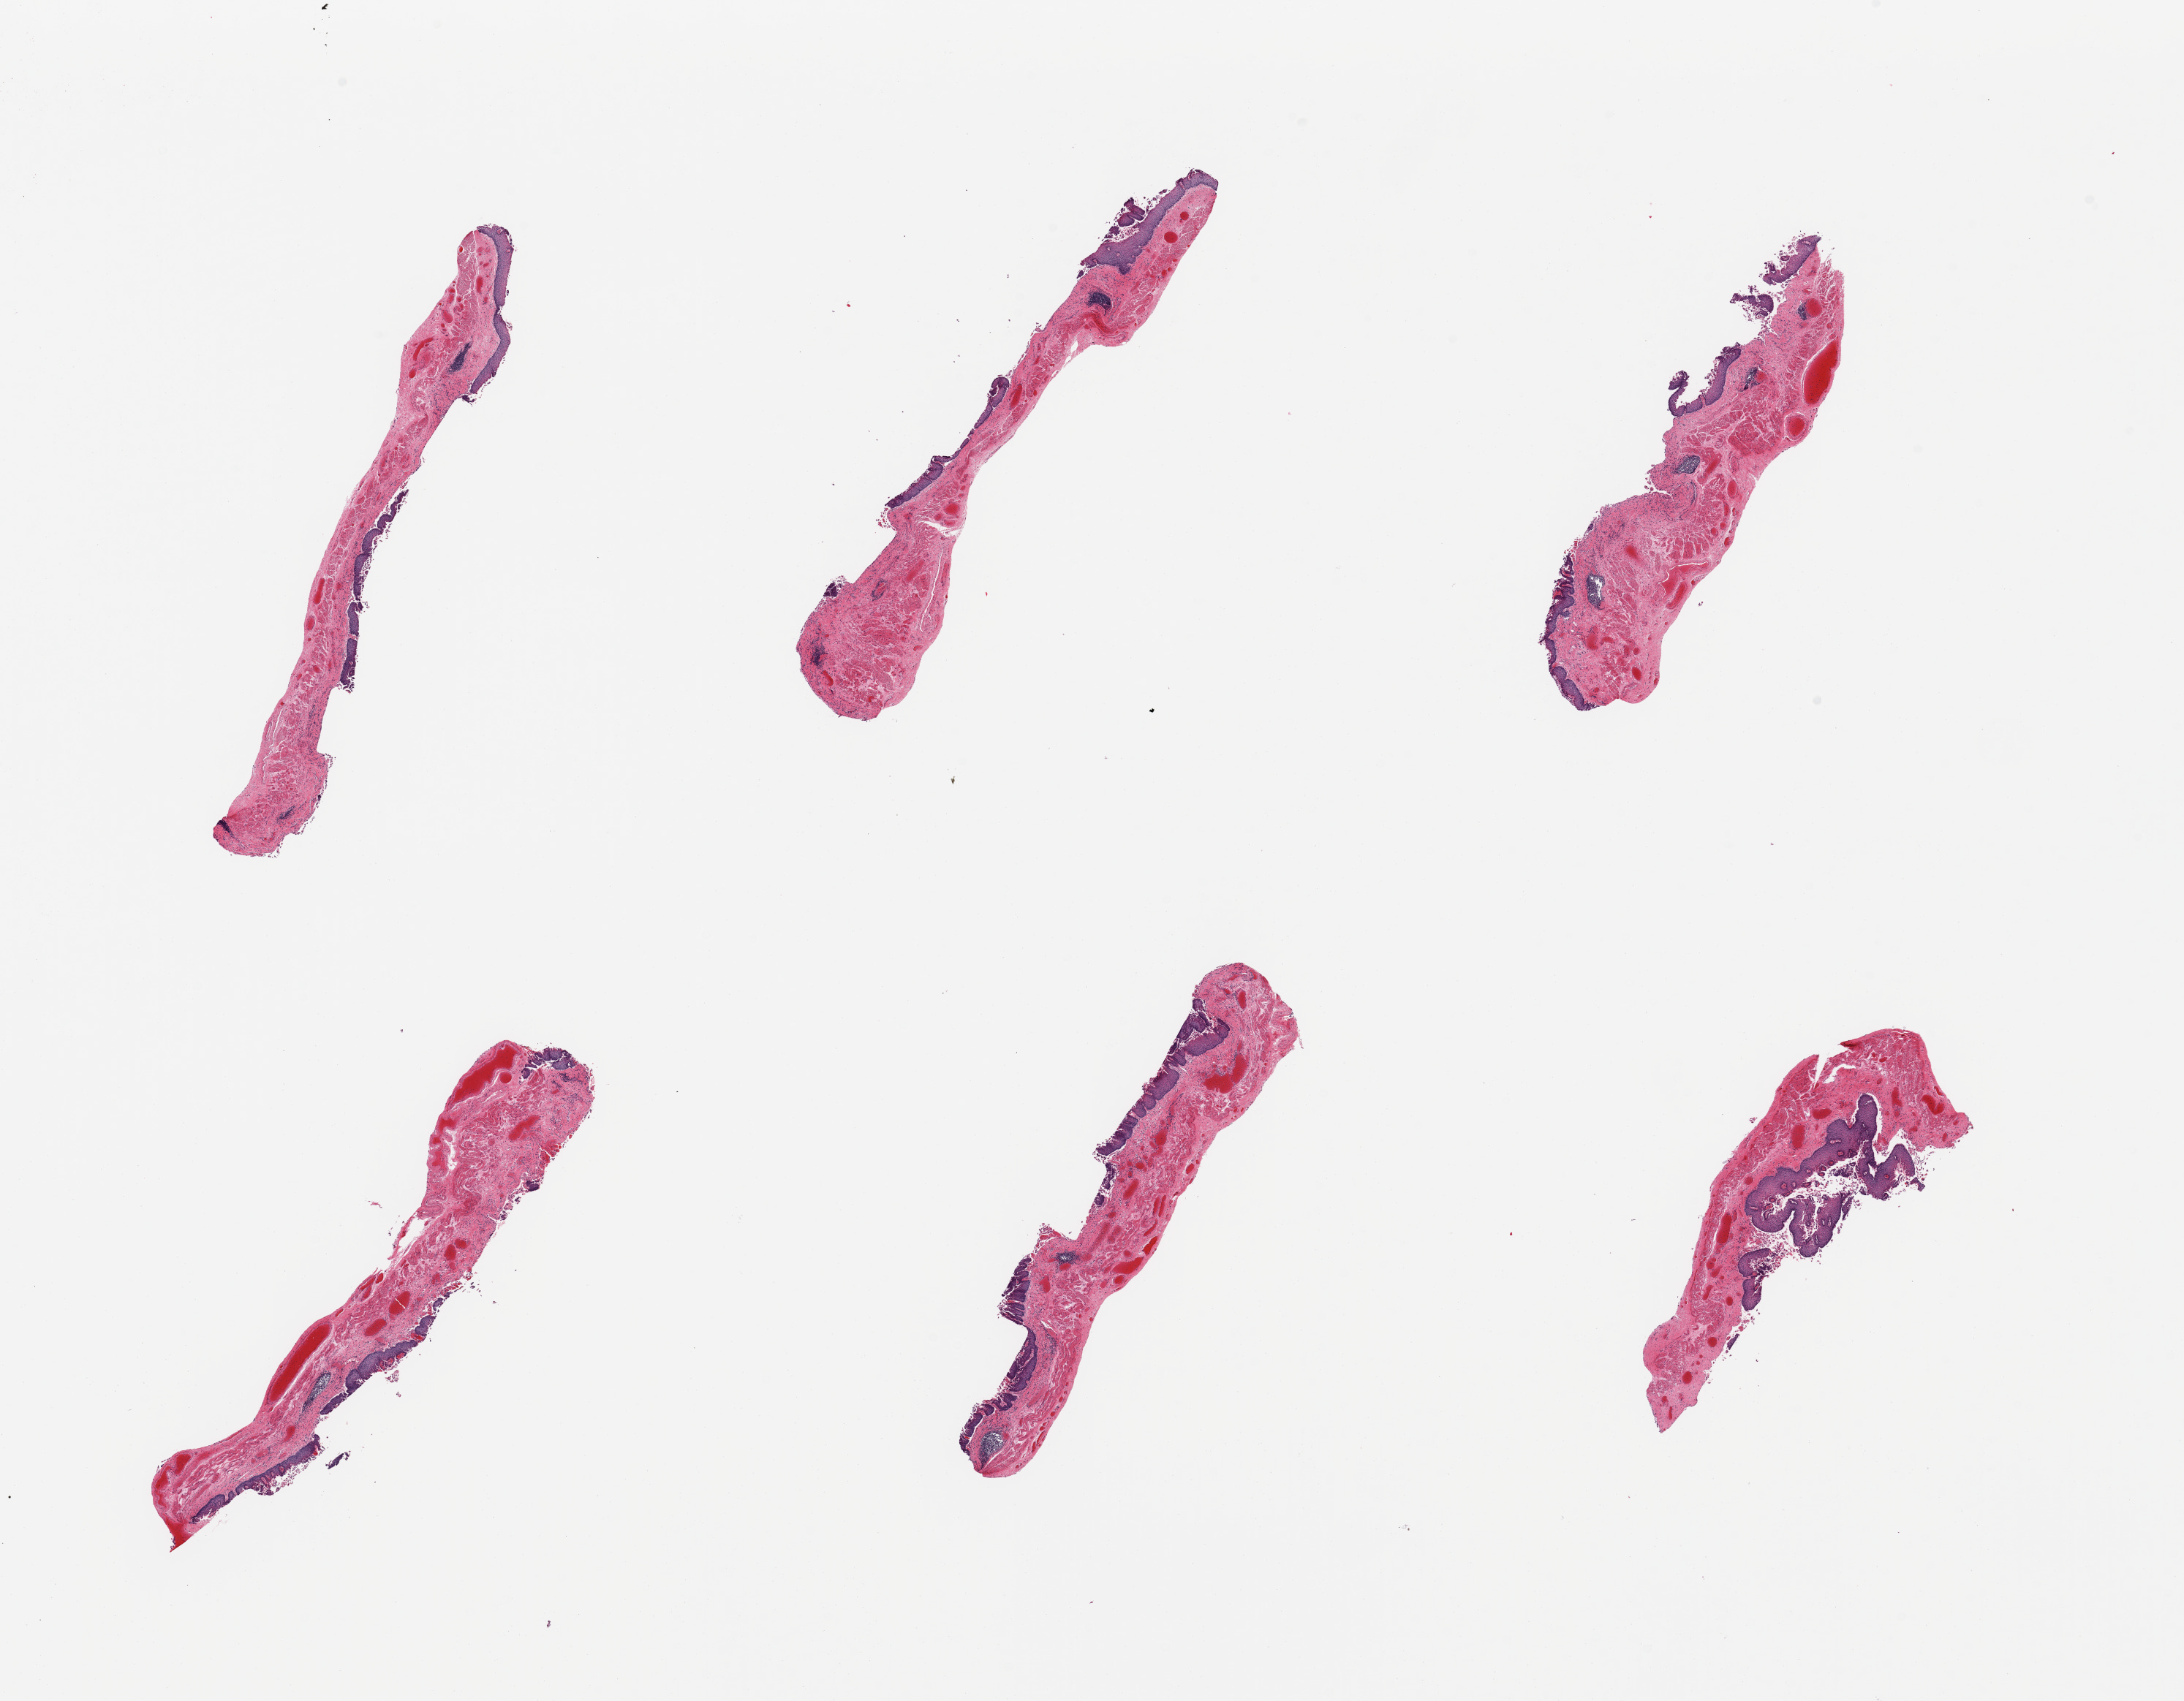
Haematoxylin and eosin whole-slide image — shown as a low-resolution overview of the whole scanned area (about 23.6 x 18.4 mm), PAXgene-fixed paraffin-embedded (PFPE) section, sampled site (target tissue): esophageal mucous membrane, donor tissue sample. Donor: female.
* pathologist's review note for this sample: 6 pieces; moderately sloughed epithelium; engorged blood vessels